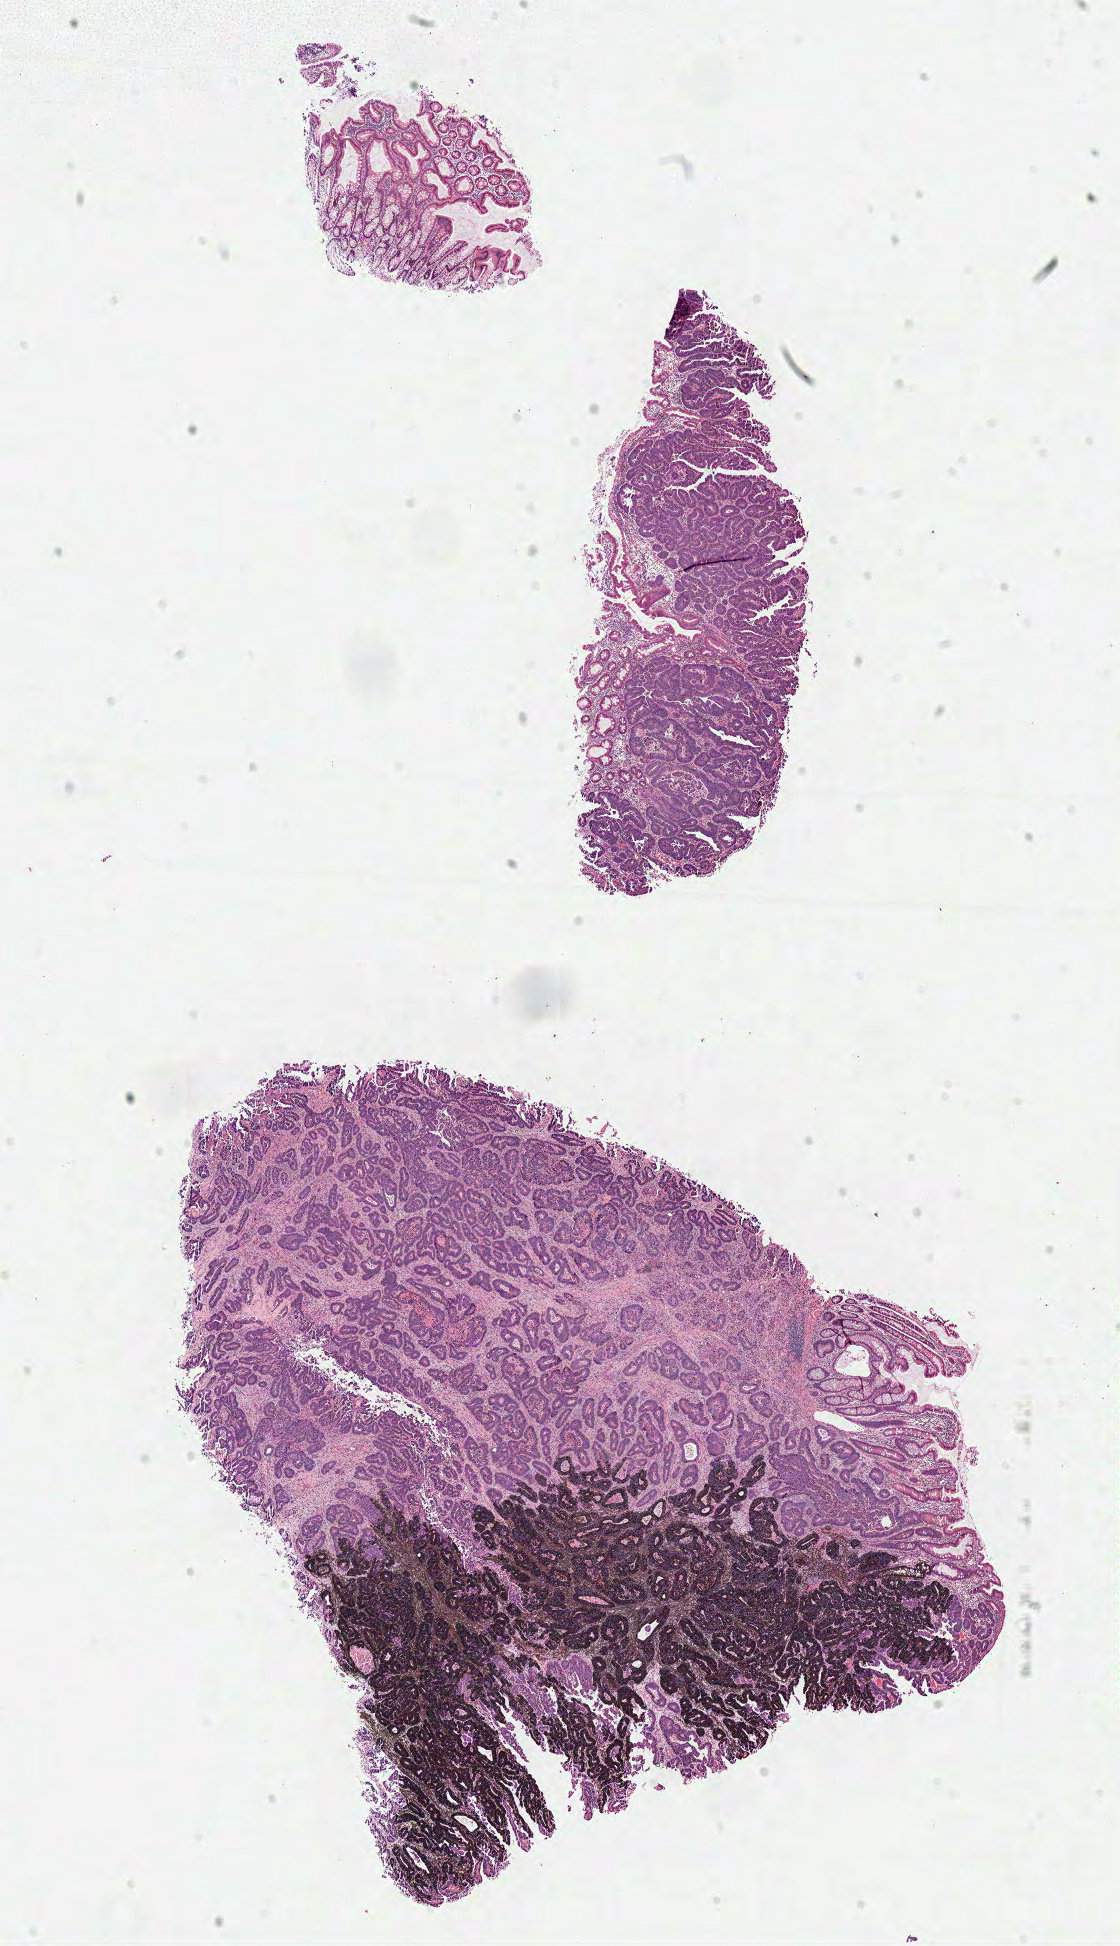
Digitized Hematoxylin and eosin (H&E) stained tissue section (whole slide), low-resolution overview of the scanned area, about 8.8 x 15.3 mm (from a 40x scan). Frozen section from the top of the tissue portion. Sample: primary tumour, colon. Male patient; age at initial diagnosis 69 years.
Pathologic diagnosis: Adenocarcinoma, NOS.